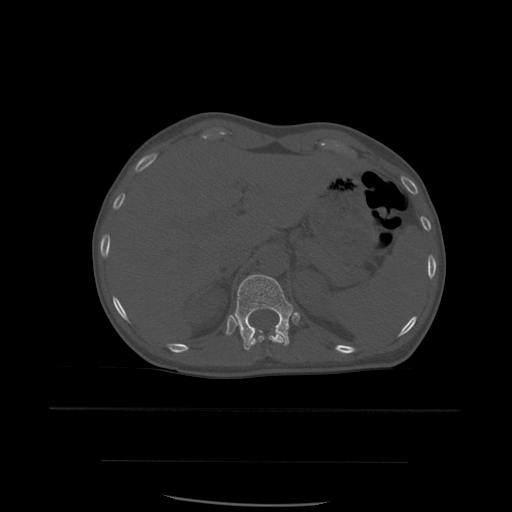
CT including the spine, one axial slice. Bone window (W 1800 / L 400 HU). 1.25 mm slice thickness. 512 × 512 image matrix, field of view 392 × 392 mm. Patient age 48 years. From the clinical record (not read from this slice): primary cancer: lung; vertebrae with lytic lesions (as recorded): T11.
Structures marked on this image (semi-automatic segmentation, software-assisted and operator-edited):
- T11 vertebra: bounding box <250,333,284,347> (left, top, right, bottom; pixels)
- T12 vertebra: <235,274,294,351>